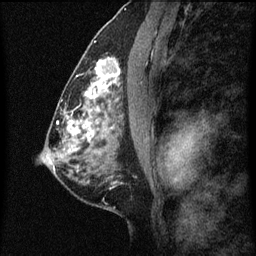
Breast MRI (dynamic contrast-enhanced), one sagittal slice. Slice 35 of 60 in the series (ordered by position). Dynamic contrast-enhanced series, image 2 of 7 at this slice position (ordered by acquisition). 1.5 T. TE 4.2 ms, TR 8 ms. 256 × 256 image matrix, field of view 180 × 180 mm. Patient: female, 51 years.
Outlined on this slice (semi-automatic segmentation, software-assisted and operator-edited):
- analysis volume of interest (the breast-tissue region the enhancement analysis was run in; not a lesion): bounding box [x1, y1, x2, y2] px = [86, 48, 123, 101]
- tumour enhancement mask (voxels above the 70 % enhancement threshold inside the analysis volume of interest): [86, 60, 121, 101]